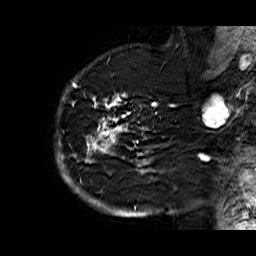
Breast MRI (dynamic contrast-enhanced), one sagittal slice. Position 49 of 60 along the scan axis. Dynamic contrast-enhanced series, time point 2 of 6 at this slice position (early post-contrast). 1.5 T. TE 6.3 ms, TR 32.9 ms. 4 mm slice thickness. 256 × 256 image matrix. Female patient. Case-level facts recorded for this patient, not image findings: setting: breast cancer imaged before/during neoadjuvant chemotherapy; receptor status: HR-positive, HER2-negative.
Annotated regions visible in this slice (semi-automatically segmented with operator editing):
- analysis volume of interest (the breast-tissue region the enhancement analysis was run in; not a lesion): bounding box <55,74,176,210> (left, top, right, bottom; pixels)
- tumour enhancement mask (voxels above the 100 % enhancement threshold inside the analysis volume of interest): <56,76,175,210>